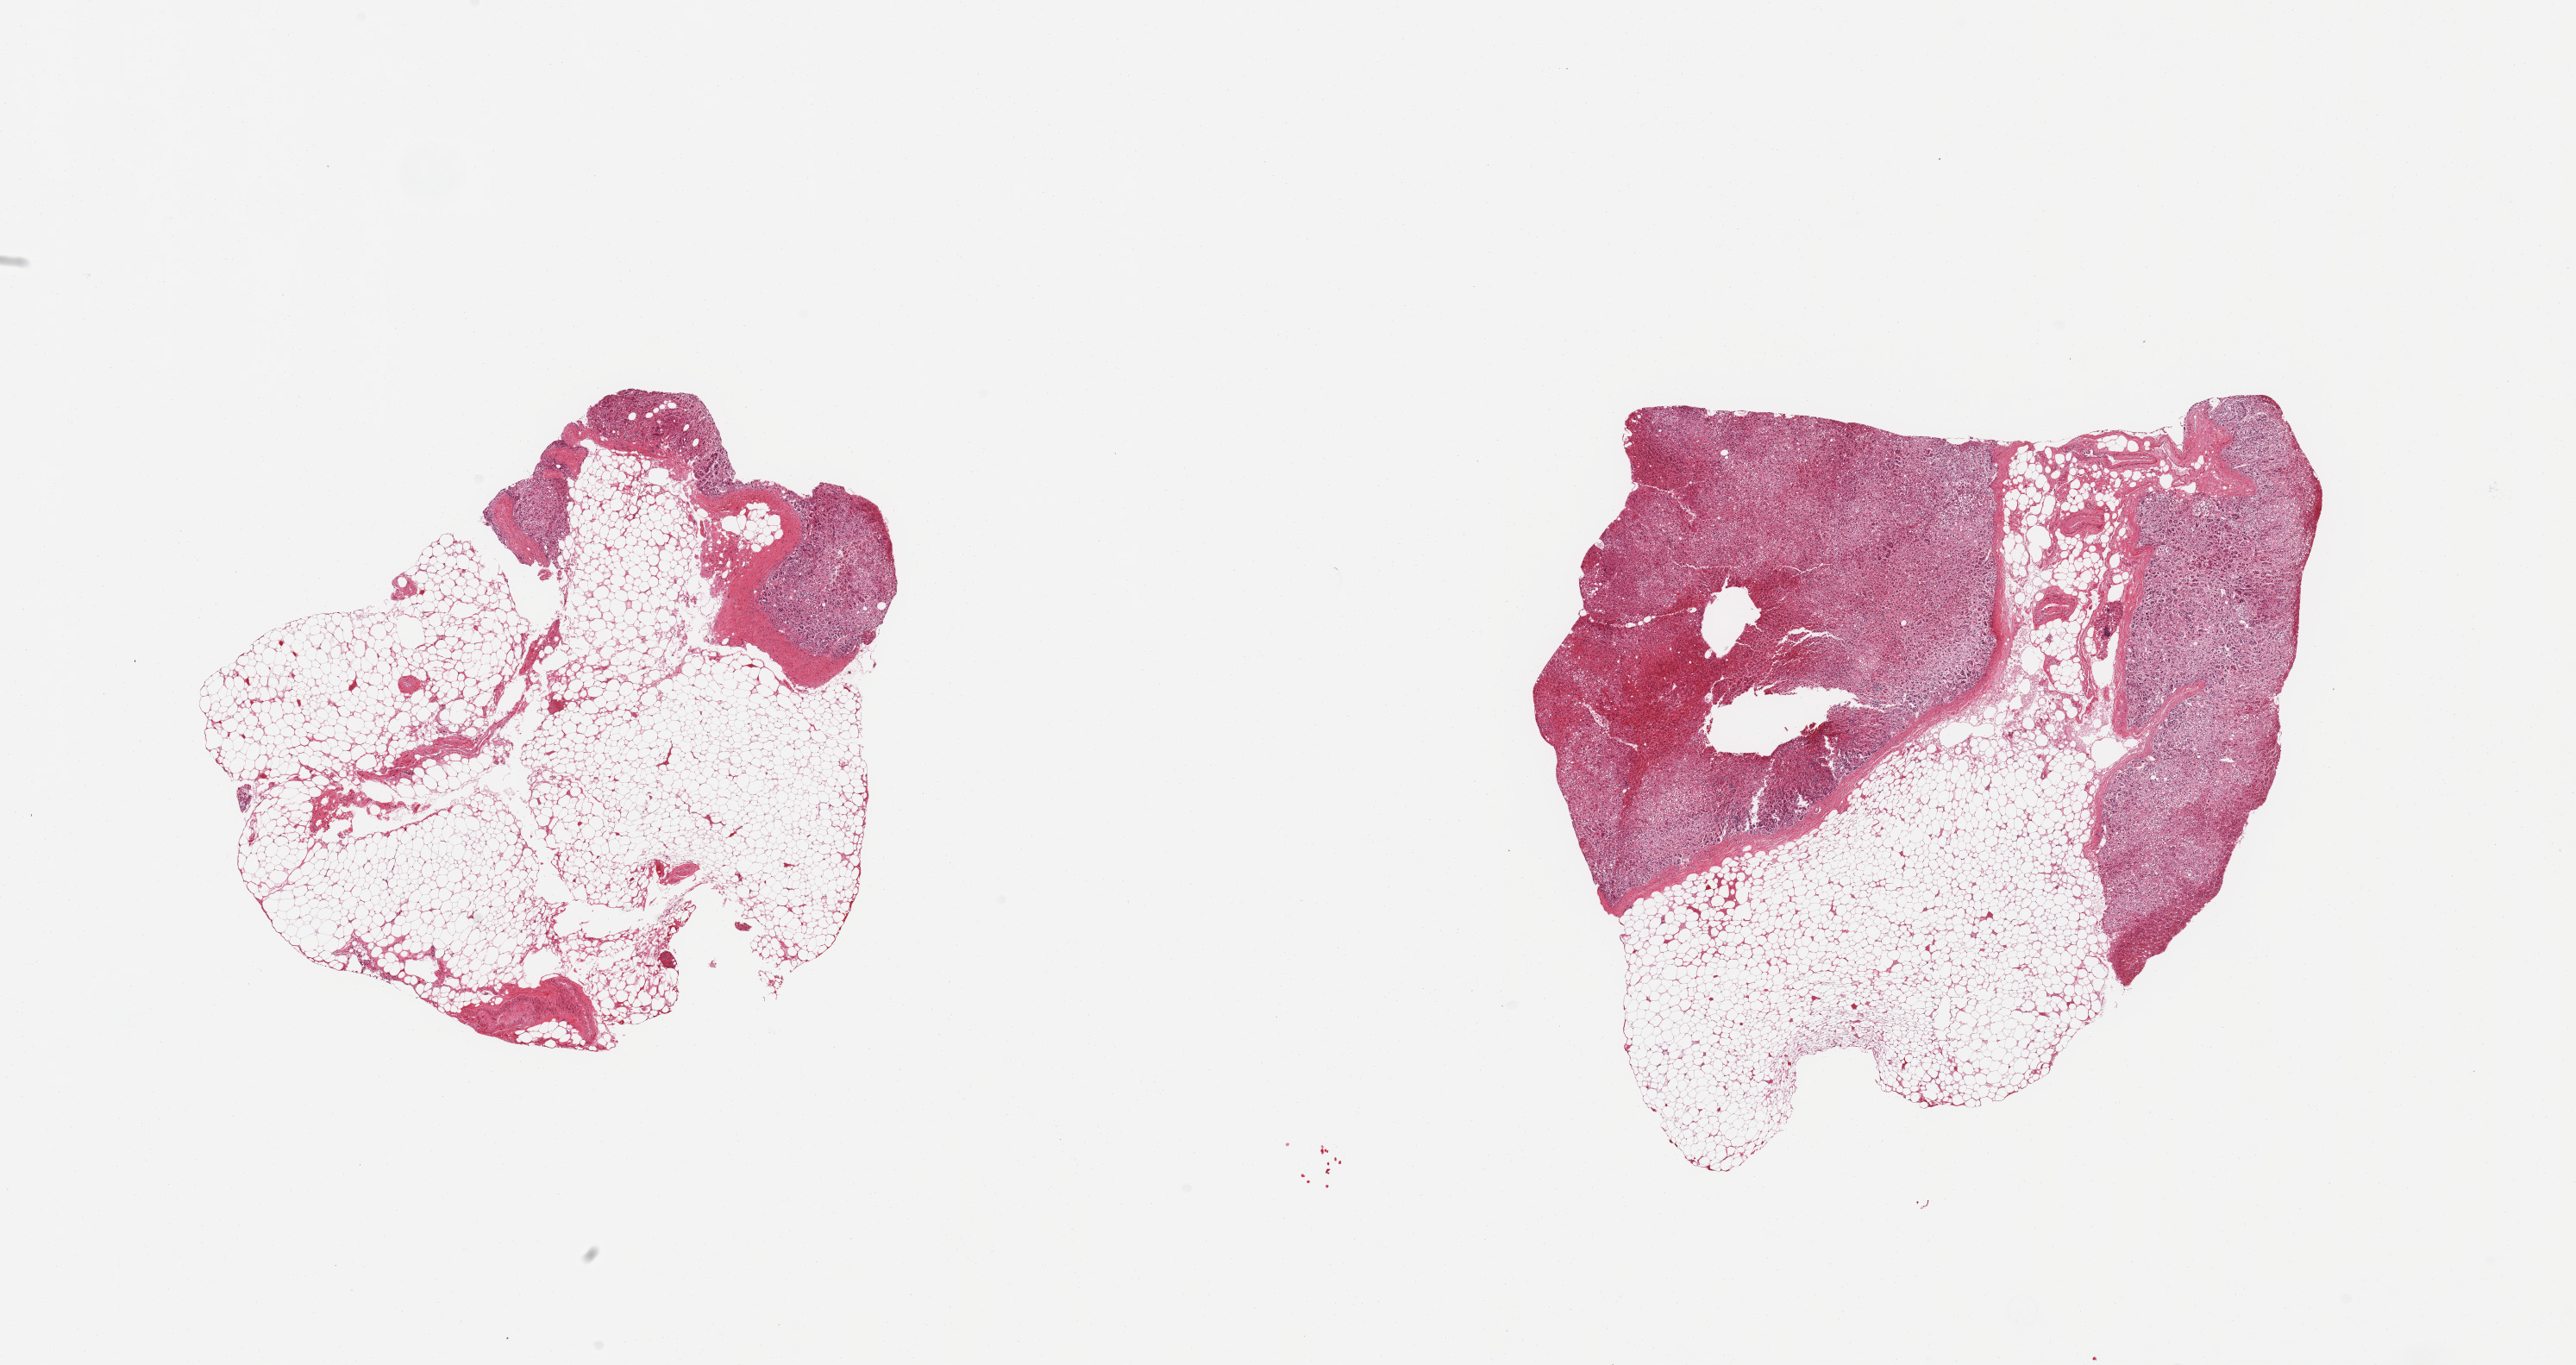
Digitized H&E-stained section, brightfield, low-resolution overview of the scanned area, about 23.6 x 12.5 mm, PAXgene-fixed, paraffin-embedded tissue, sampled site (target tissue): adrenal gland, donor tissue sample. Donor: male.
Review note (as recorded): 2 pieces; moderately and focally severly autolyzed adrenal cortex; 90% and 40% external fat.